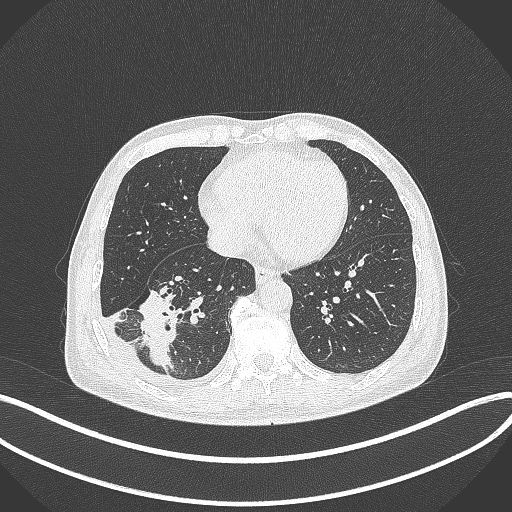
Chest CT, one axial slice. Slice 129 of 388 in the series (ordered by position). Reconstruction kernel B70f. Lung window (W 1500 / L -600 HU). 1 mm slice thickness. 512 × 512 image matrix, field of view 400 × 400 mm. Patient: male, 64 years. From the clinical record (not read from this slice): clinical TNM (as recorded): T3 N0 M0; histopathological grade: G2-3.
Annotated regions visible in this slice (bounding box drawn by a radiologist):
- lung tumour (recorded histology: adenocarcinoma): bounding box [x1, y1, x2, y2] px = [137, 287, 176, 375]